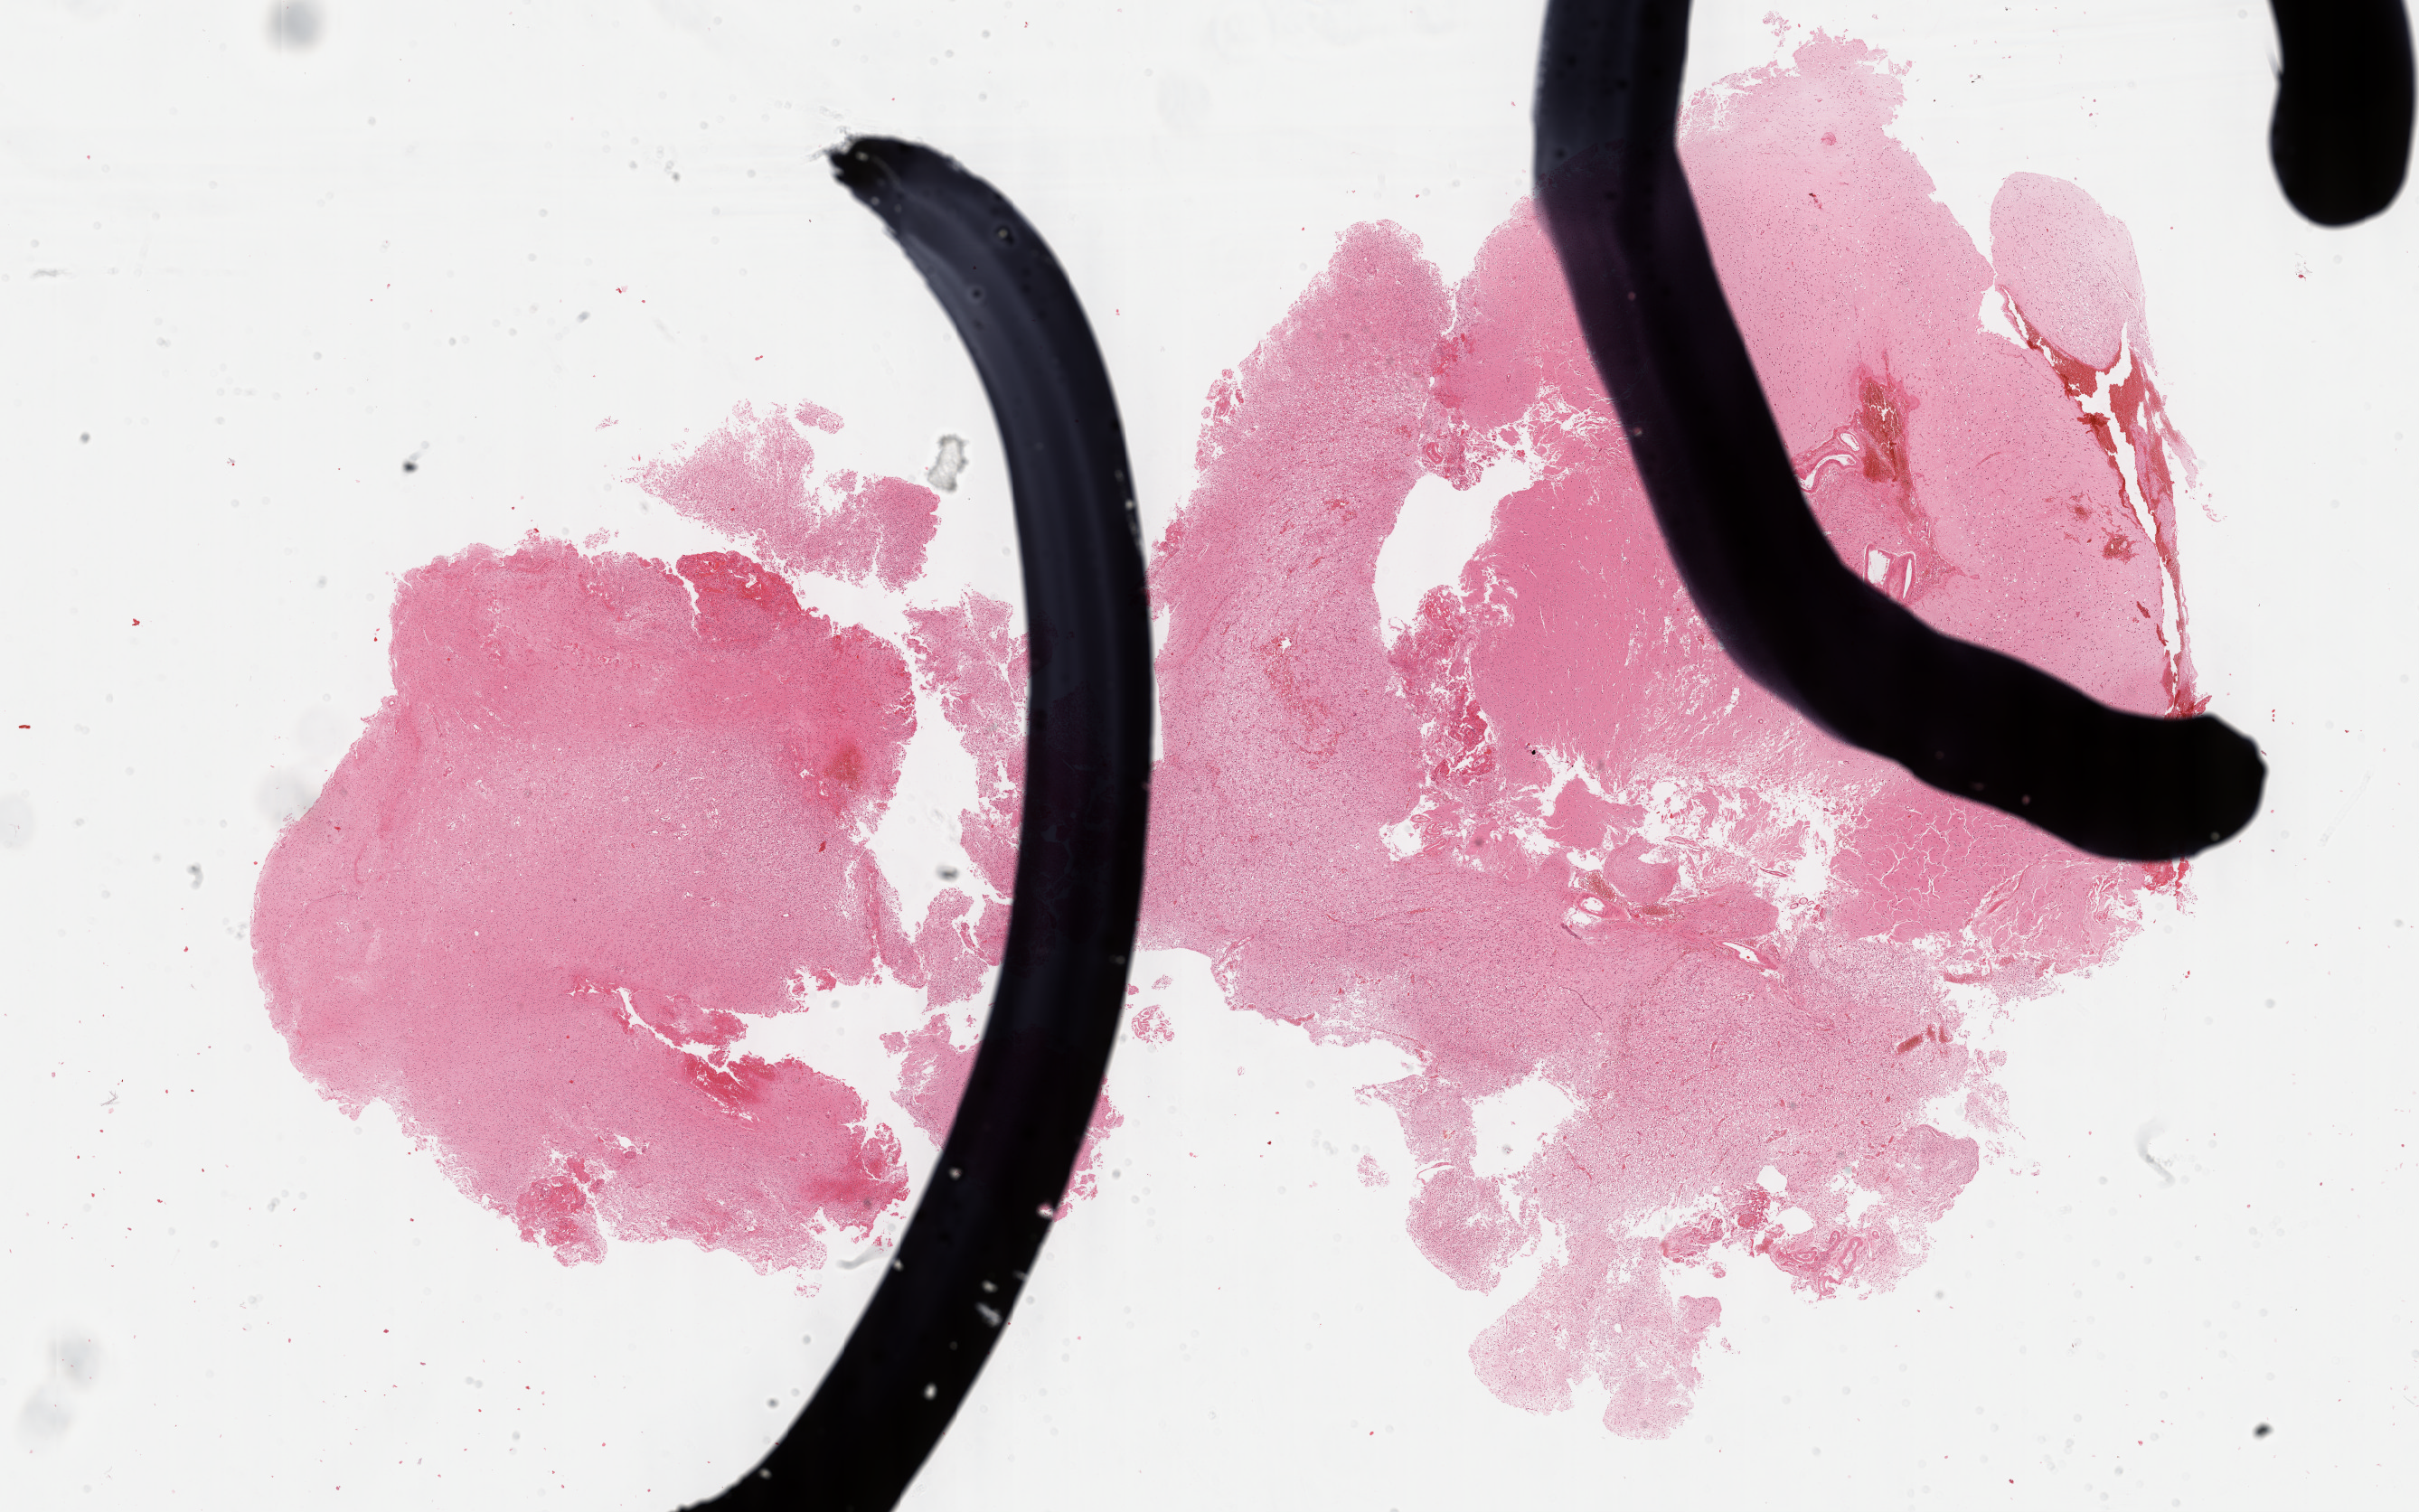
Whole-slide histology image, H&E-stained — a low-resolution overview of the entire scanned area, about 21.6 x 13.5 mm (from a 40x scan); formalin-fixed paraffin-embedded (FFPE) diagnostic section; primary tumour sample from the brain. Male patient; age at initial diagnosis 52 years. Histologic grade: G3 (poorly differentiated).
Pathologic diagnosis: Astrocytoma, anaplastic (cerebrum).